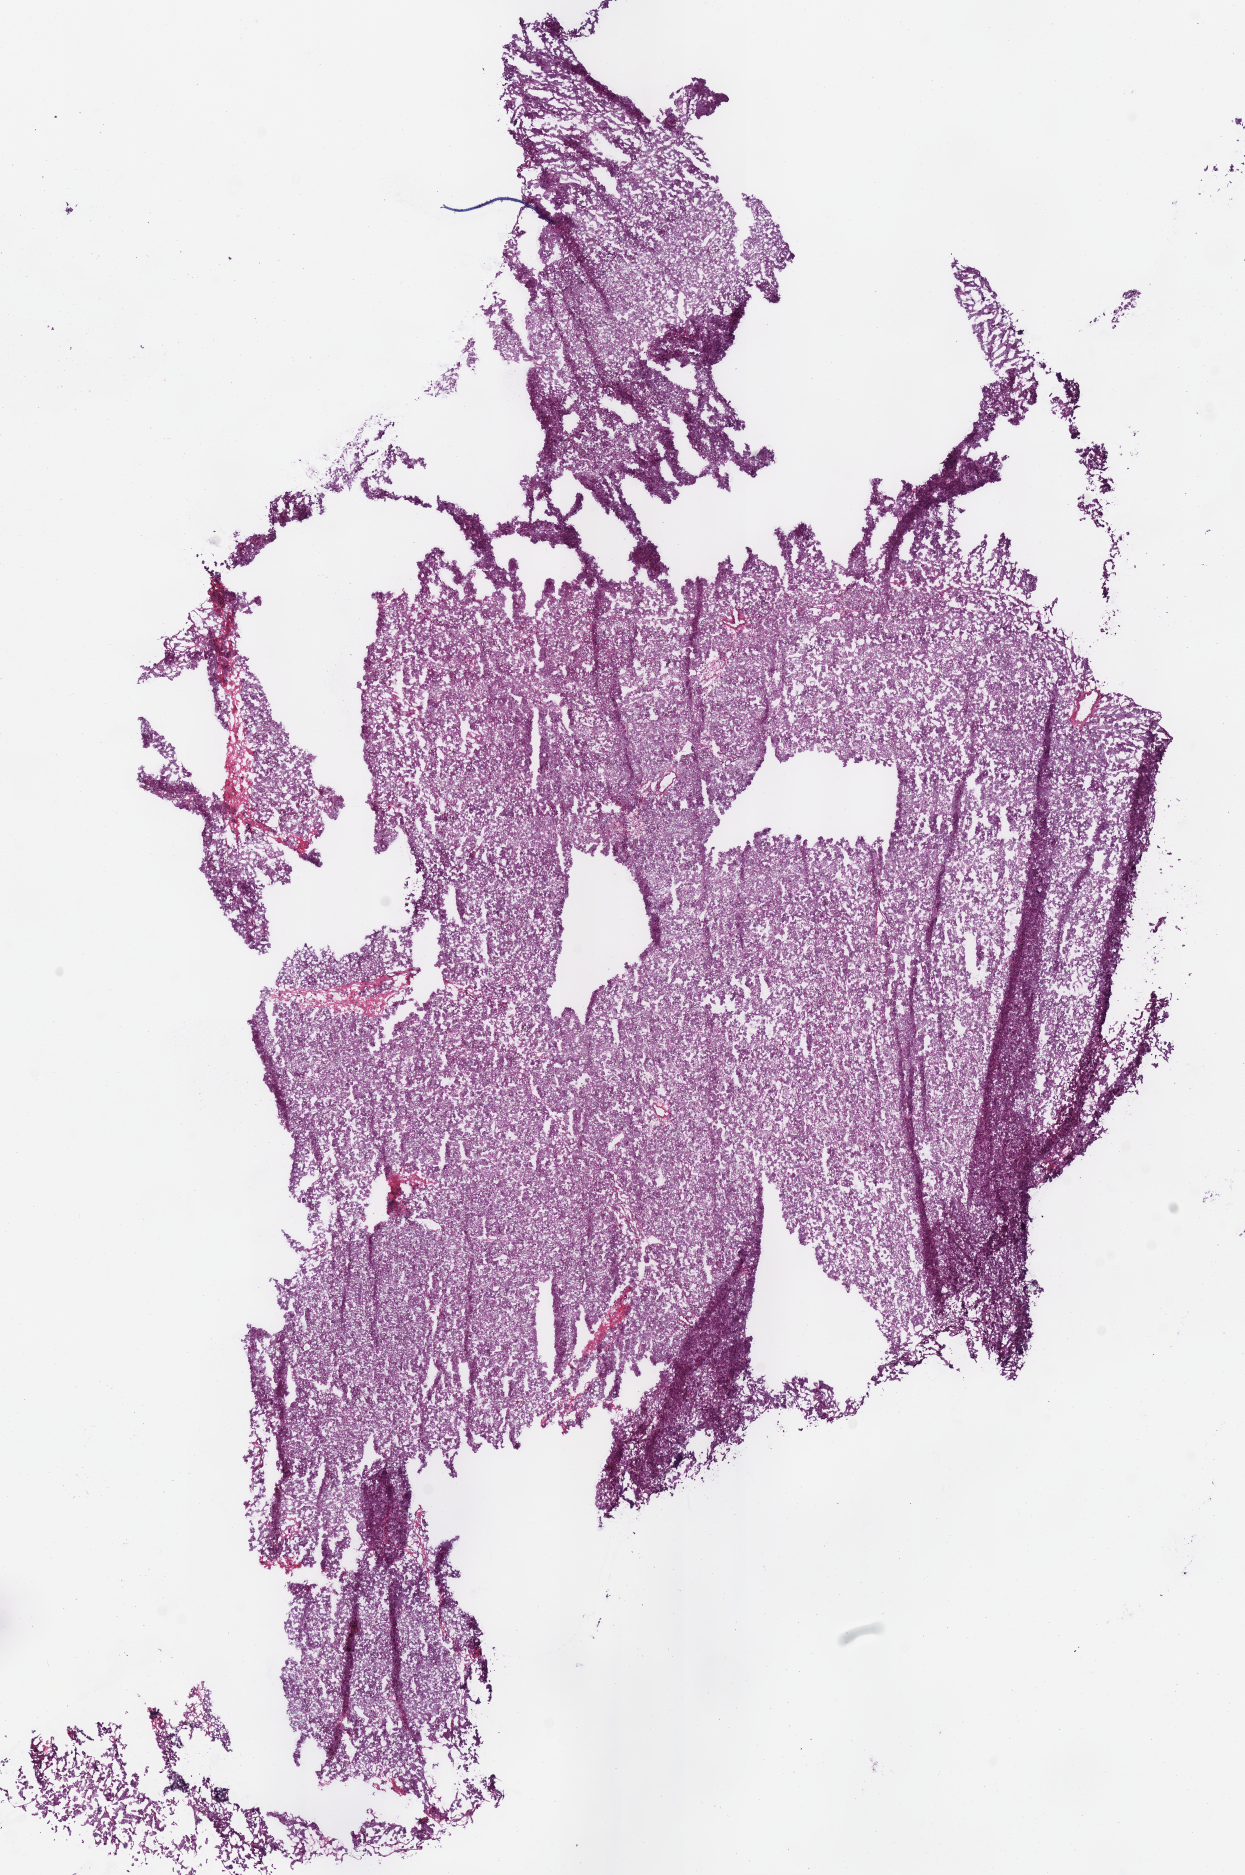
Whole-slide histology image, Hematoxylin and eosin (H&E) stained, low-resolution overview of the scanned area, about 9.8 x 14.7 mm (slide scanned at 40x); frozen section from the bottom of the tissue portion; primary tumour sample from the kidney. Patient: male, age at initial diagnosis 29 years. Slide review estimates, as recorded: tumour cells 90%, tumour nuclei 90%, normal cells 0%, stromal cells 10%, necrosis 0%.
* AJCC pathologic stage: III (7th edition)
* laterality: left
* diagnosis: Renal cell carcinoma, chromophobe type